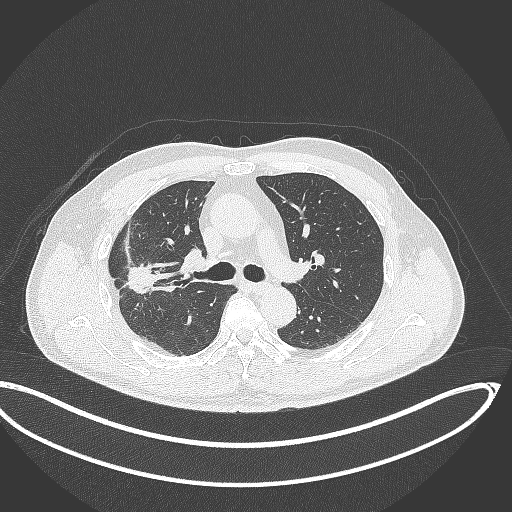
Chest CT, one axial slice; slice 219 of 391 in the series (ordered by position); 120 kVp; lung window (W 1500 / L -600 HU); 512 × 512 image matrix, field of view 439 × 439 mm. Male patient, age 63 years. Case-level facts recorded for this patient, not image findings: clinical TNM (as recorded): T1c N0 M0; histopathological grade: G2-3.
Outlined on this slice (bounding box drawn by a radiologist):
- lung tumour (recorded histology: adenocarcinoma): bounding box [x1, y1, x2, y2] px = [123, 257, 159, 303]